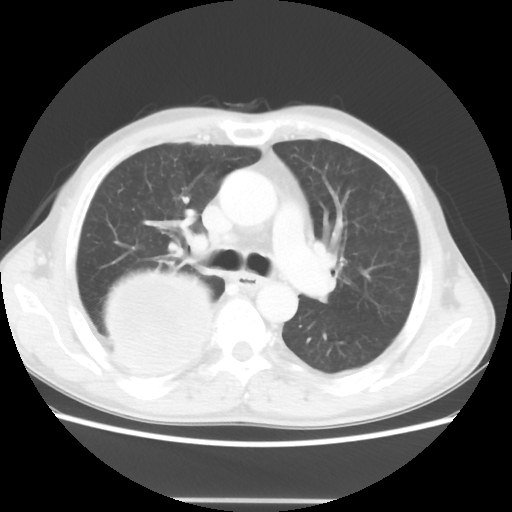
Chest CT, one axial slice; position 31 of 48 along the scan axis; reconstruction kernel STANDARD; 100 kVp; lung window (W 1500 / L -600 HU); 5 mm slice thickness; 512 × 512 image matrix, field of view 361 × 361 mm. Male patient, age 66 years. Case-level facts recorded for this patient, not image findings: clinical TNM (as recorded): T4 N1 M1; histopathological grade: G3.
Annotated regions visible in this slice (rectangle marked by the reading radiologist):
- lung tumour (recorded histology: small cell carcinoma): bounding box [x1, y1, x2, y2] px = [106, 262, 219, 389]